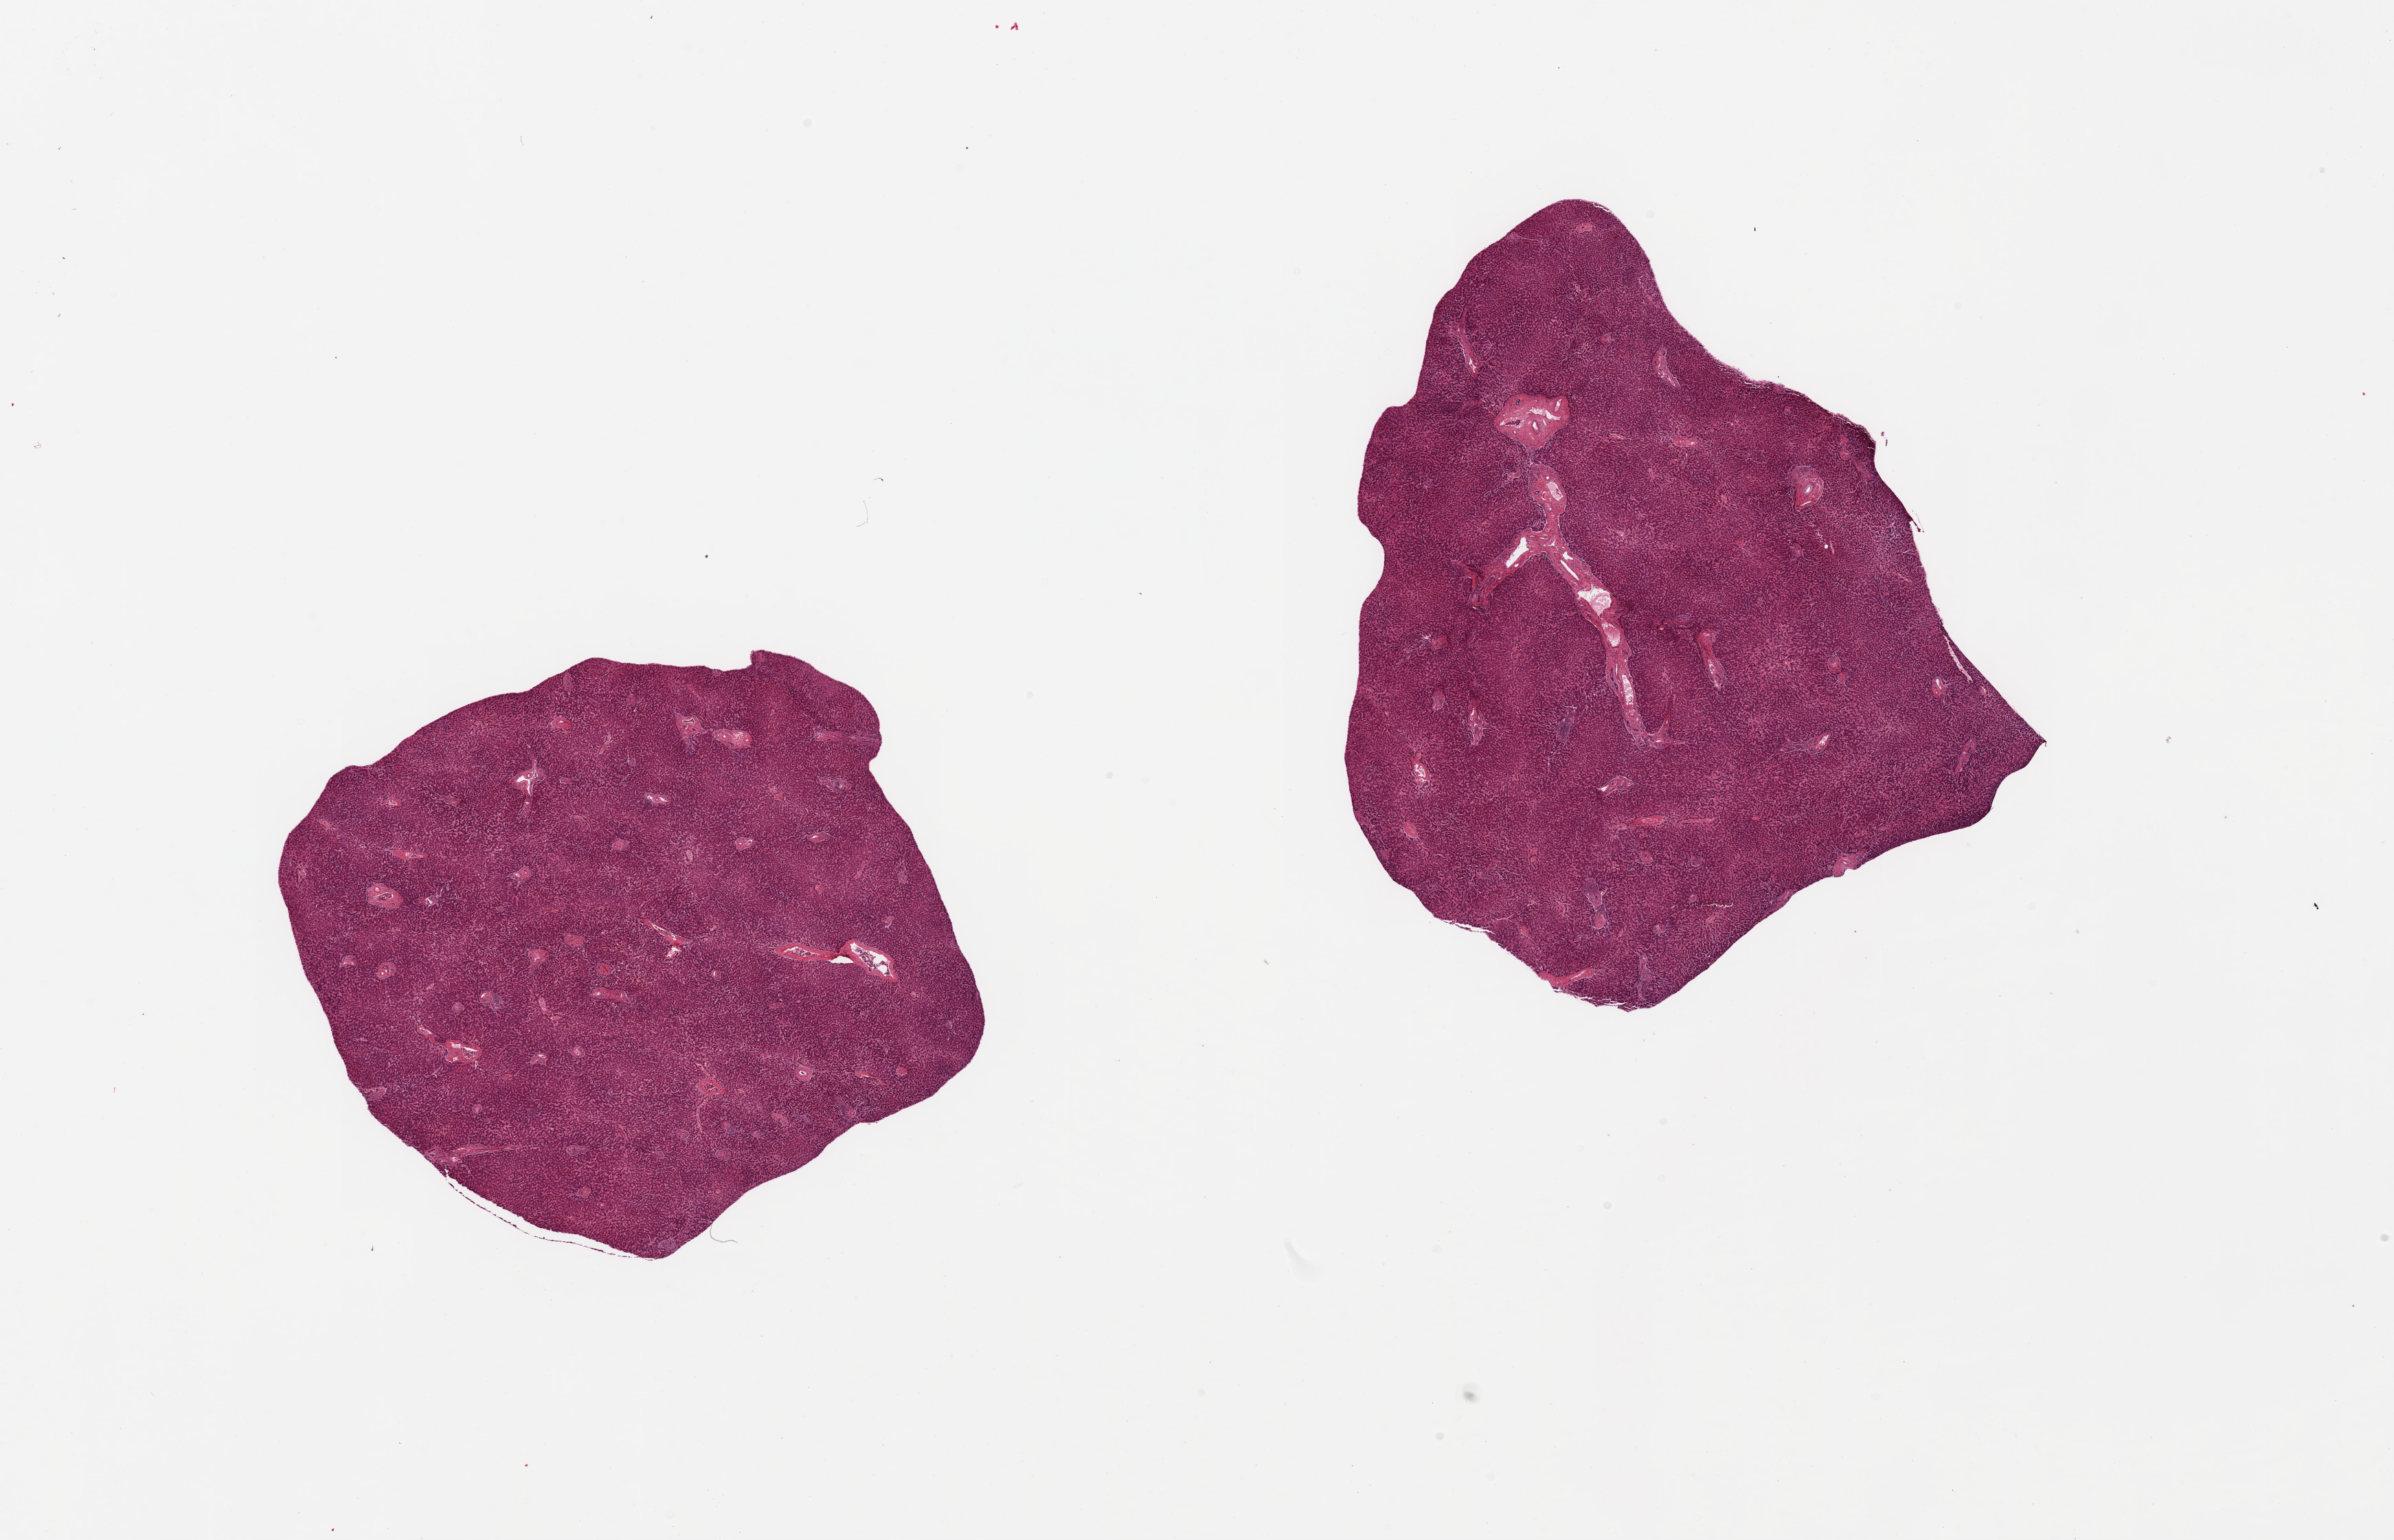
H&E whole-slide image, brightfield, whole scanned area (about 27.6 x 17.7 mm, acquisition: 20x scan) shown as a low-resolution overview, PAXgene-fixed paraffin-embedded (PFPE) section, sampled site (target tissue): liver, tissue donor sample. Donor: female.
Review note (as recorded): 2 pieces; congestion; focal predominantly portal chronic inflammation.